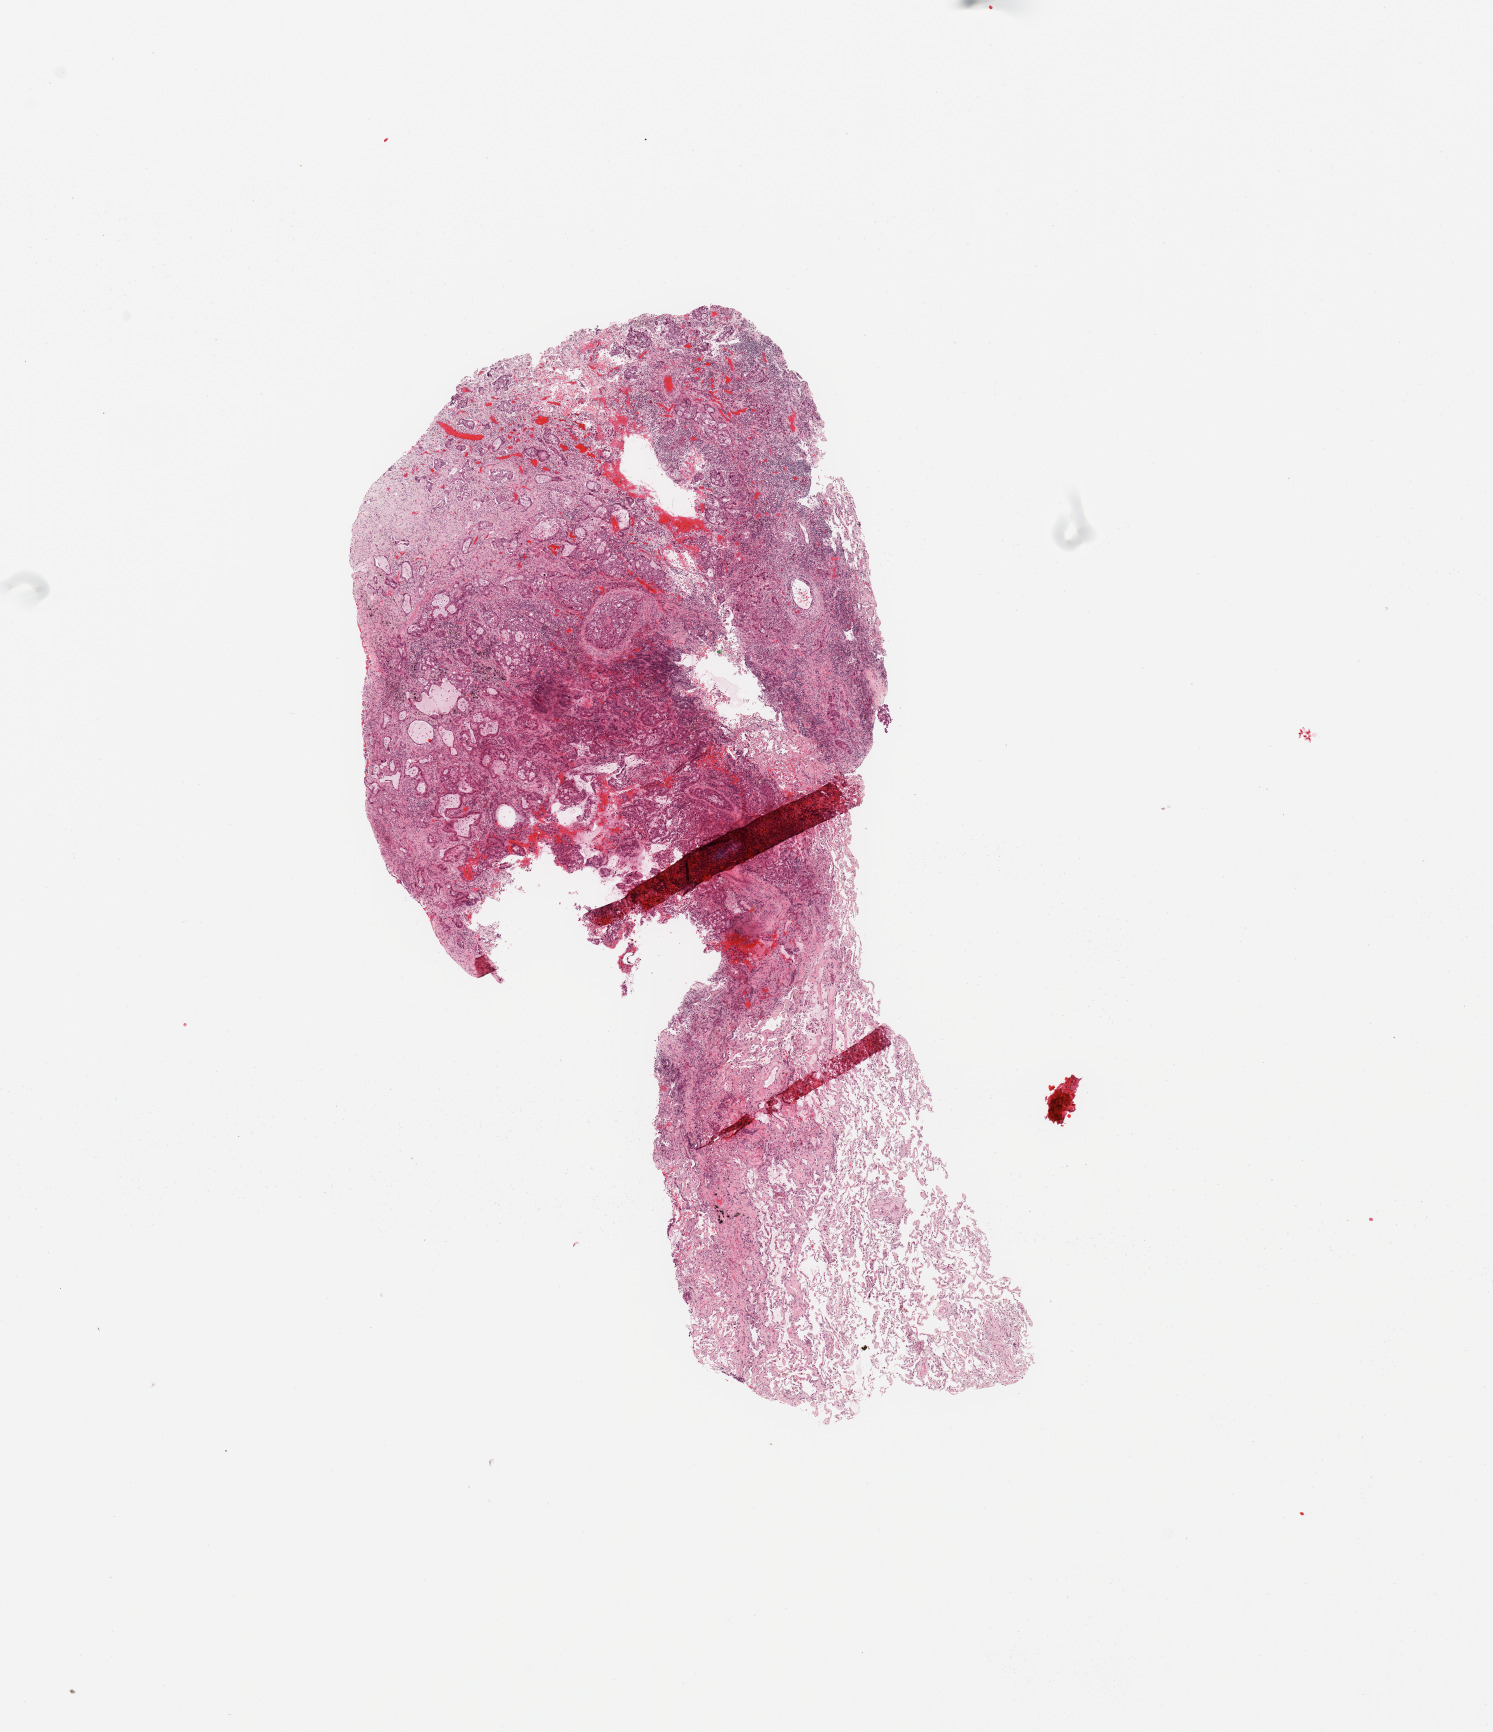
Digitized Hematoxylin and eosin (H&E) stained tissue section (whole slide) — shown as a low-resolution overview of the whole scanned area (about 11.8 x 13.7 mm). Tumour tissue sample, sampled site: lung. Male, 66 y/o. Histologic grade: G2 (moderately differentiated). Slide review estimates, as recorded: tumour nuclei 60%, necrosis 7%.
Diagnosis: Adenocarcinoma, NOS. AJCC pathologic stage: IIIA.